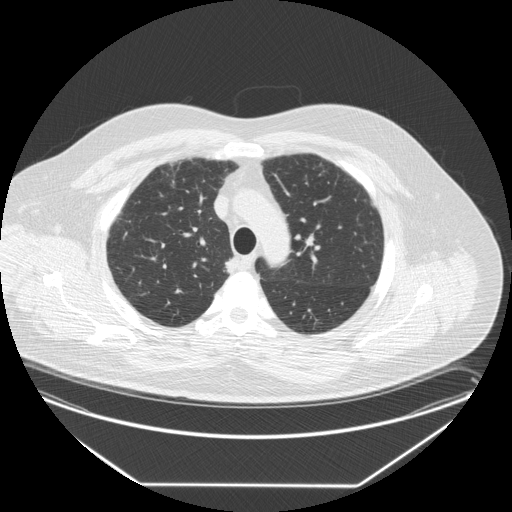
Low-dose screening chest CT, one axial slice. Slice 204 of 258 in the series (ordered by position). Lung window (W 1500 / L -600 HU). 512 × 512 image matrix, field of view 440 × 440 mm.
Outlined on this slice (outlined manually by an expert reader):
- lesion 1 (tumor, upper lobe of right lung): box from (x=225, y=258) to (x=235, y=271) px